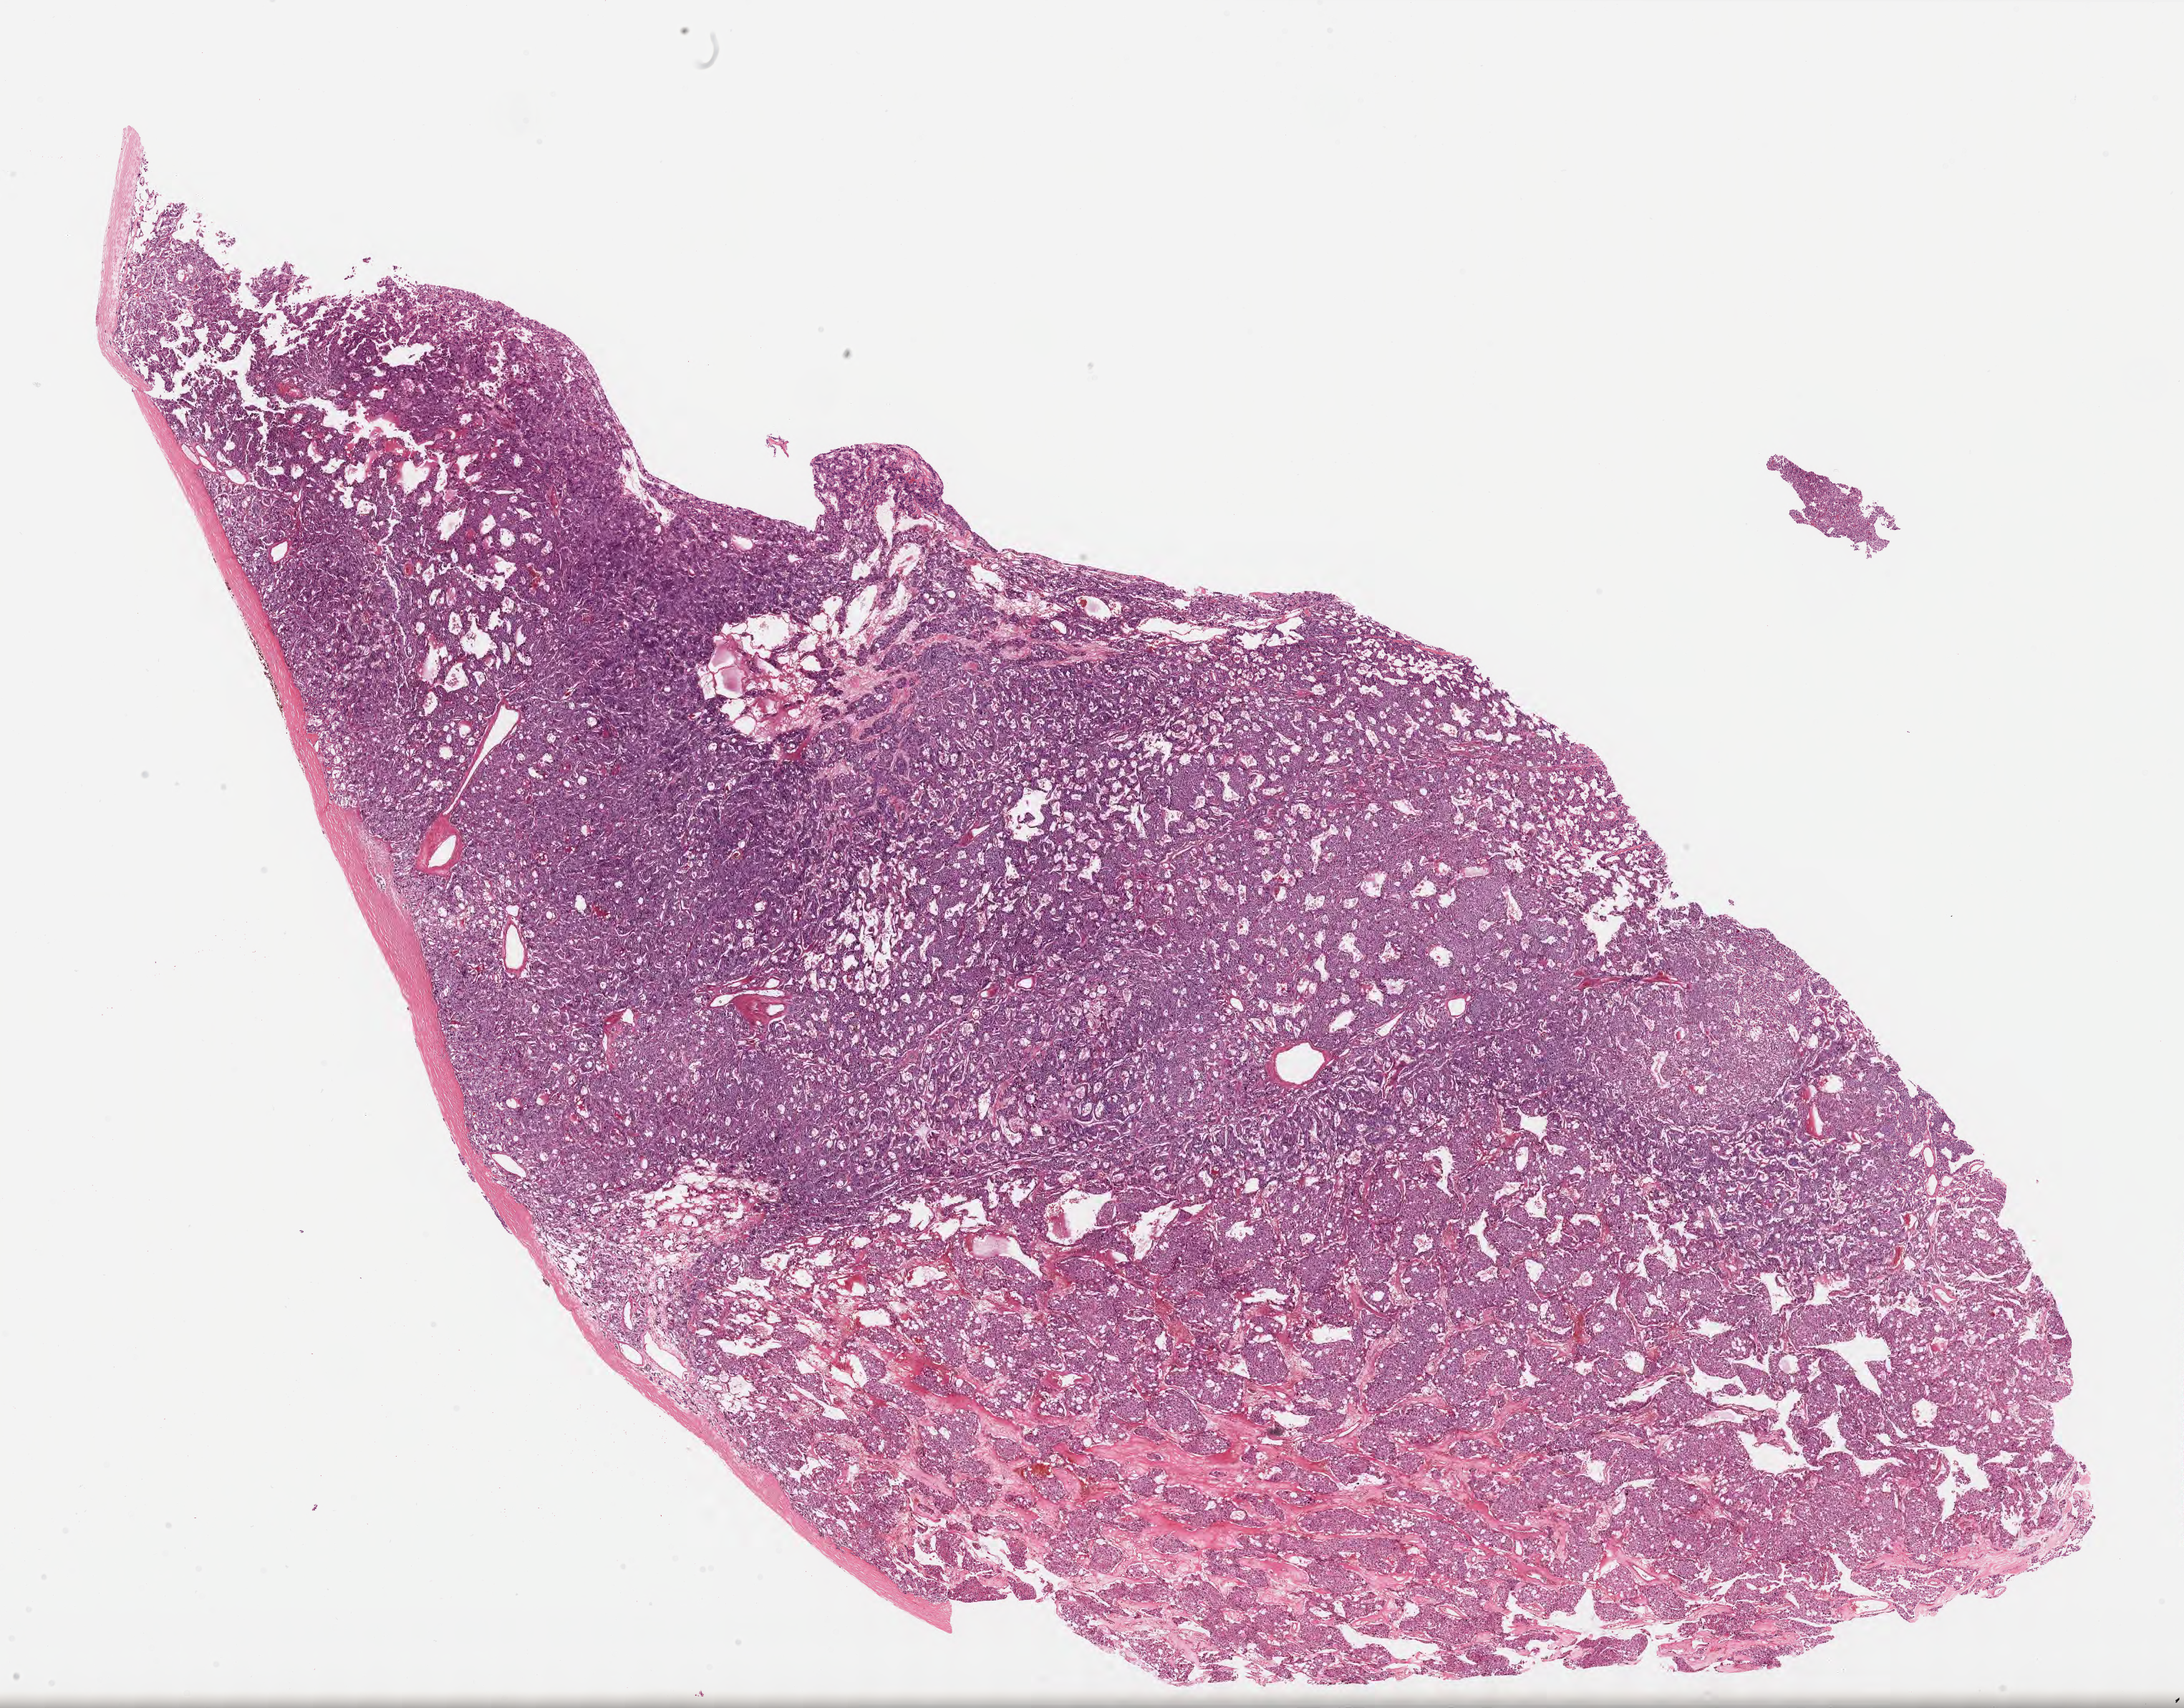
Whole-slide histology image, H&E, low-resolution overview of the scanned area, about 24.0 x 18.8 mm (acquisition: 40x scan). Formalin-fixed paraffin-embedded (FFPE) diagnostic section. Adrenal gland, primary tumour sample. Female patient; age at initial diagnosis 71 years.
• diagnosis: Pheochromocytoma, NOS